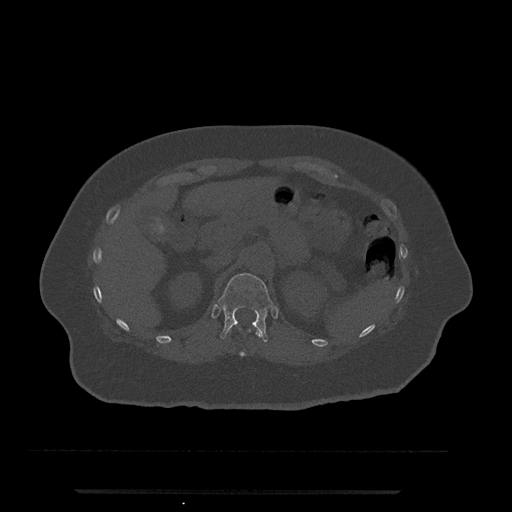
CT including the spine, one axial slice; position 185 of 797 along the scan axis; reconstruction kernel Br40s/3; bone window (W 1800 / L 400 HU); 0.5 mm slice thickness; 512 × 512 image matrix, field of view 440 × 440 mm. Female patient, age 51 years. Case-level facts recorded for this patient, not image findings: primary cancer: neuro; vertebrae with lytic lesions (as recorded): T8.
Annotated regions visible in this slice (semi-automatic segmentation, software-assisted and operator-edited):
- T11 vertebra: bounding box <229,329,261,357> (left, top, right, bottom; pixels)
- T12 vertebra: <218,273,273,342>